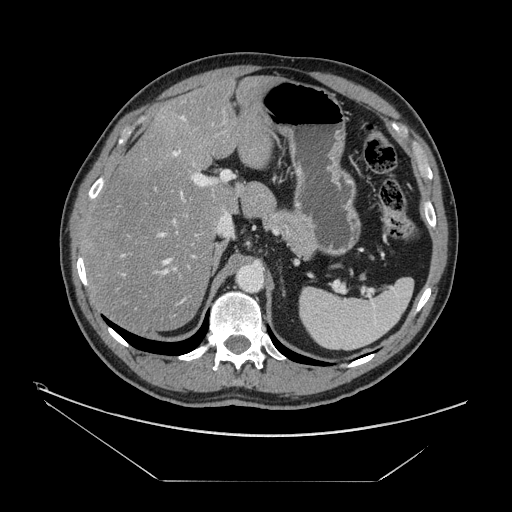
Contrast-enhanced abdominal CT, one axial slice. Slice 96 of 161 in the series (ordered by position). Reconstruction kernel STANDARD. 120 kVp. Intravenous contrast given. Soft-tissue window (W 400 / L 40 HU). 2.5 mm slice thickness. 512 × 512 image matrix, field of view 440 × 440 mm. Male patient, age 65 years. Case-level facts recorded for this patient, not image findings: diagnosis: colorectal cancer liver metastases, imaged before liver resection; multiple liver metastases: yes; largest metastasis: 4.2 cm; disease in both lobes: yes.
Annotated regions visible in this slice (expert manual segmentation):
- hepatic veins: bounding box [x1, y1, x2, y2] px = [121, 117, 184, 277]
- liver: [85, 78, 274, 330]
- planned liver remnant (the part of the liver to remain after resection): [85, 78, 274, 330]
- portal vein (with intrahepatic branches): [117, 150, 230, 316]